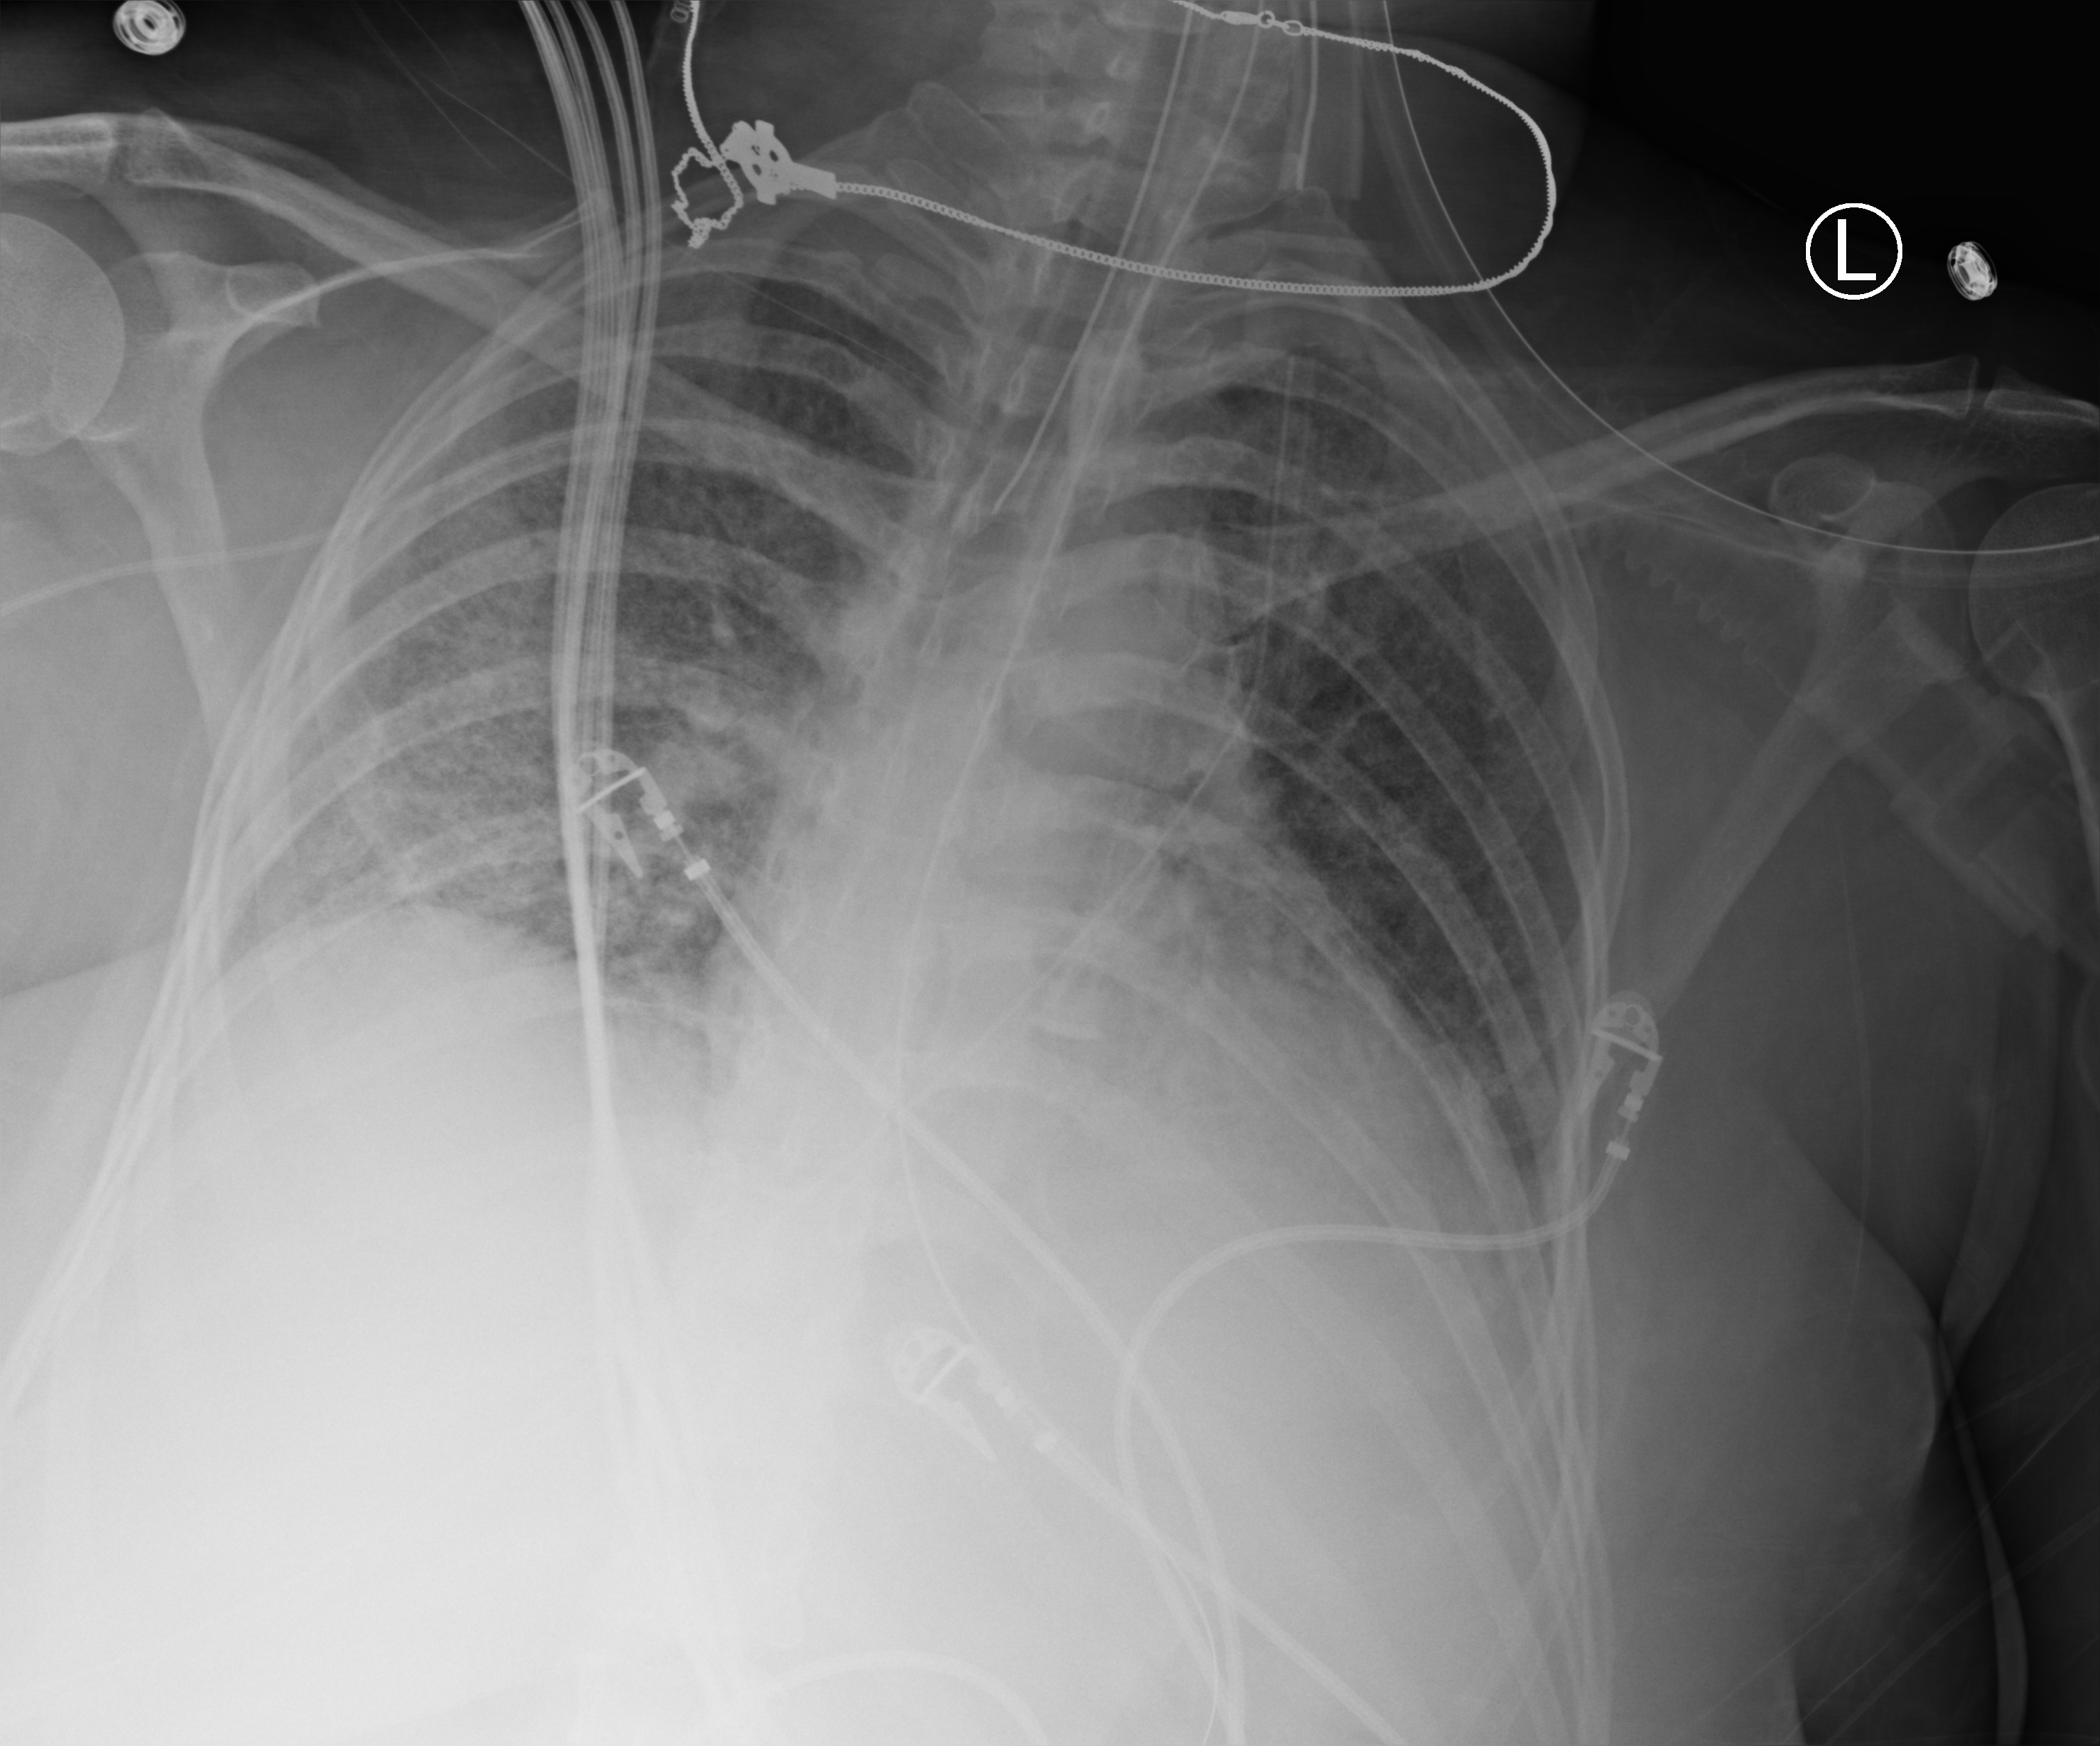
Chest X-ray (portable). Female patient hospitalised with COVID-19, age 18–59 years.
Hospital-stay facts (about this admission, not read from this image; timing relative to this image not recorded):
- diabetes (admission record): no